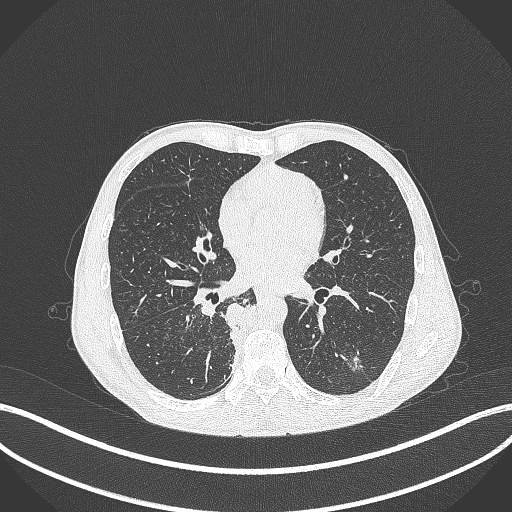
Chest CT, one axial slice. Position 175 of 371 along the scan axis. Reconstruction kernel B70f. 120 kVp. Lung window (W 1500 / L -600 HU). 1 mm slice thickness. 512 × 512 image matrix, field of view 400 × 400 mm. Patient: male, 58 years. Case-level facts recorded for this patient, not image findings: clinical TNM (as recorded): T3 N1 M1.
Outlined on this slice (rectangle marked by the reading radiologist):
- lung tumour (recorded histology: squamous cell carcinoma): bounding box (x1, y1, x2, y2) in pixels: (219, 296, 253, 336)